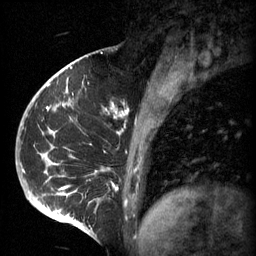
Breast MRI (dynamic contrast-enhanced), one sagittal slice. Slice 22 of 60 in the series (ordered by position). 3 images stored at this slice position (order not interpretable as contrast timing). 1.5 T. TE 4.2 ms, TR 11 ms. 256 × 256 image matrix, field of view 200 × 200 mm. Female patient, age 51 years.
Outlined on this slice (semi-automatically segmented with operator editing):
- analysis volume of interest (the breast-tissue region the enhancement analysis was run in; not a lesion): box from (x=48, y=82) to (x=161, y=197) px
- tumour enhancement mask (voxels above the 70 % enhancement threshold inside the analysis volume of interest): (x=48, y=82)–(x=161, y=195)